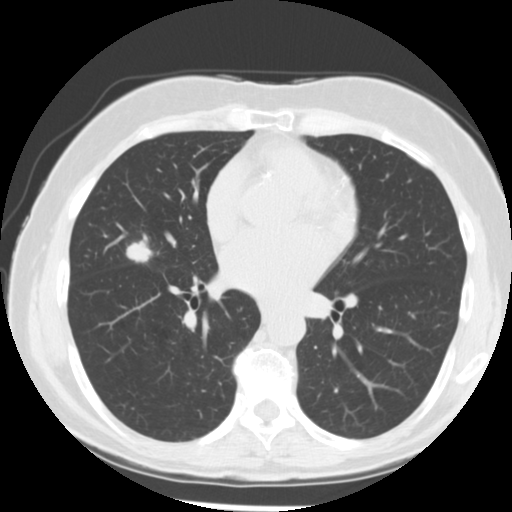
Low-dose screening chest CT, axial slice, baseline screening round, lung window (W 1500 / L -600 HU), 2.5 mm slice thickness. Female participant, aged 66 years at enrolment. Former smoker at enrolment.
• Expert-annotated lung lesion, bounding box <120,234,164,269> (left, top, right, bottom; pixels).
• Reader record for this screening exam (exam-level; its link to the box is not recorded): non-calcified nodule or mass ≥4 mm, right middle lobe, 15 × 13 mm, poorly defined margins, soft tissue attenuation.